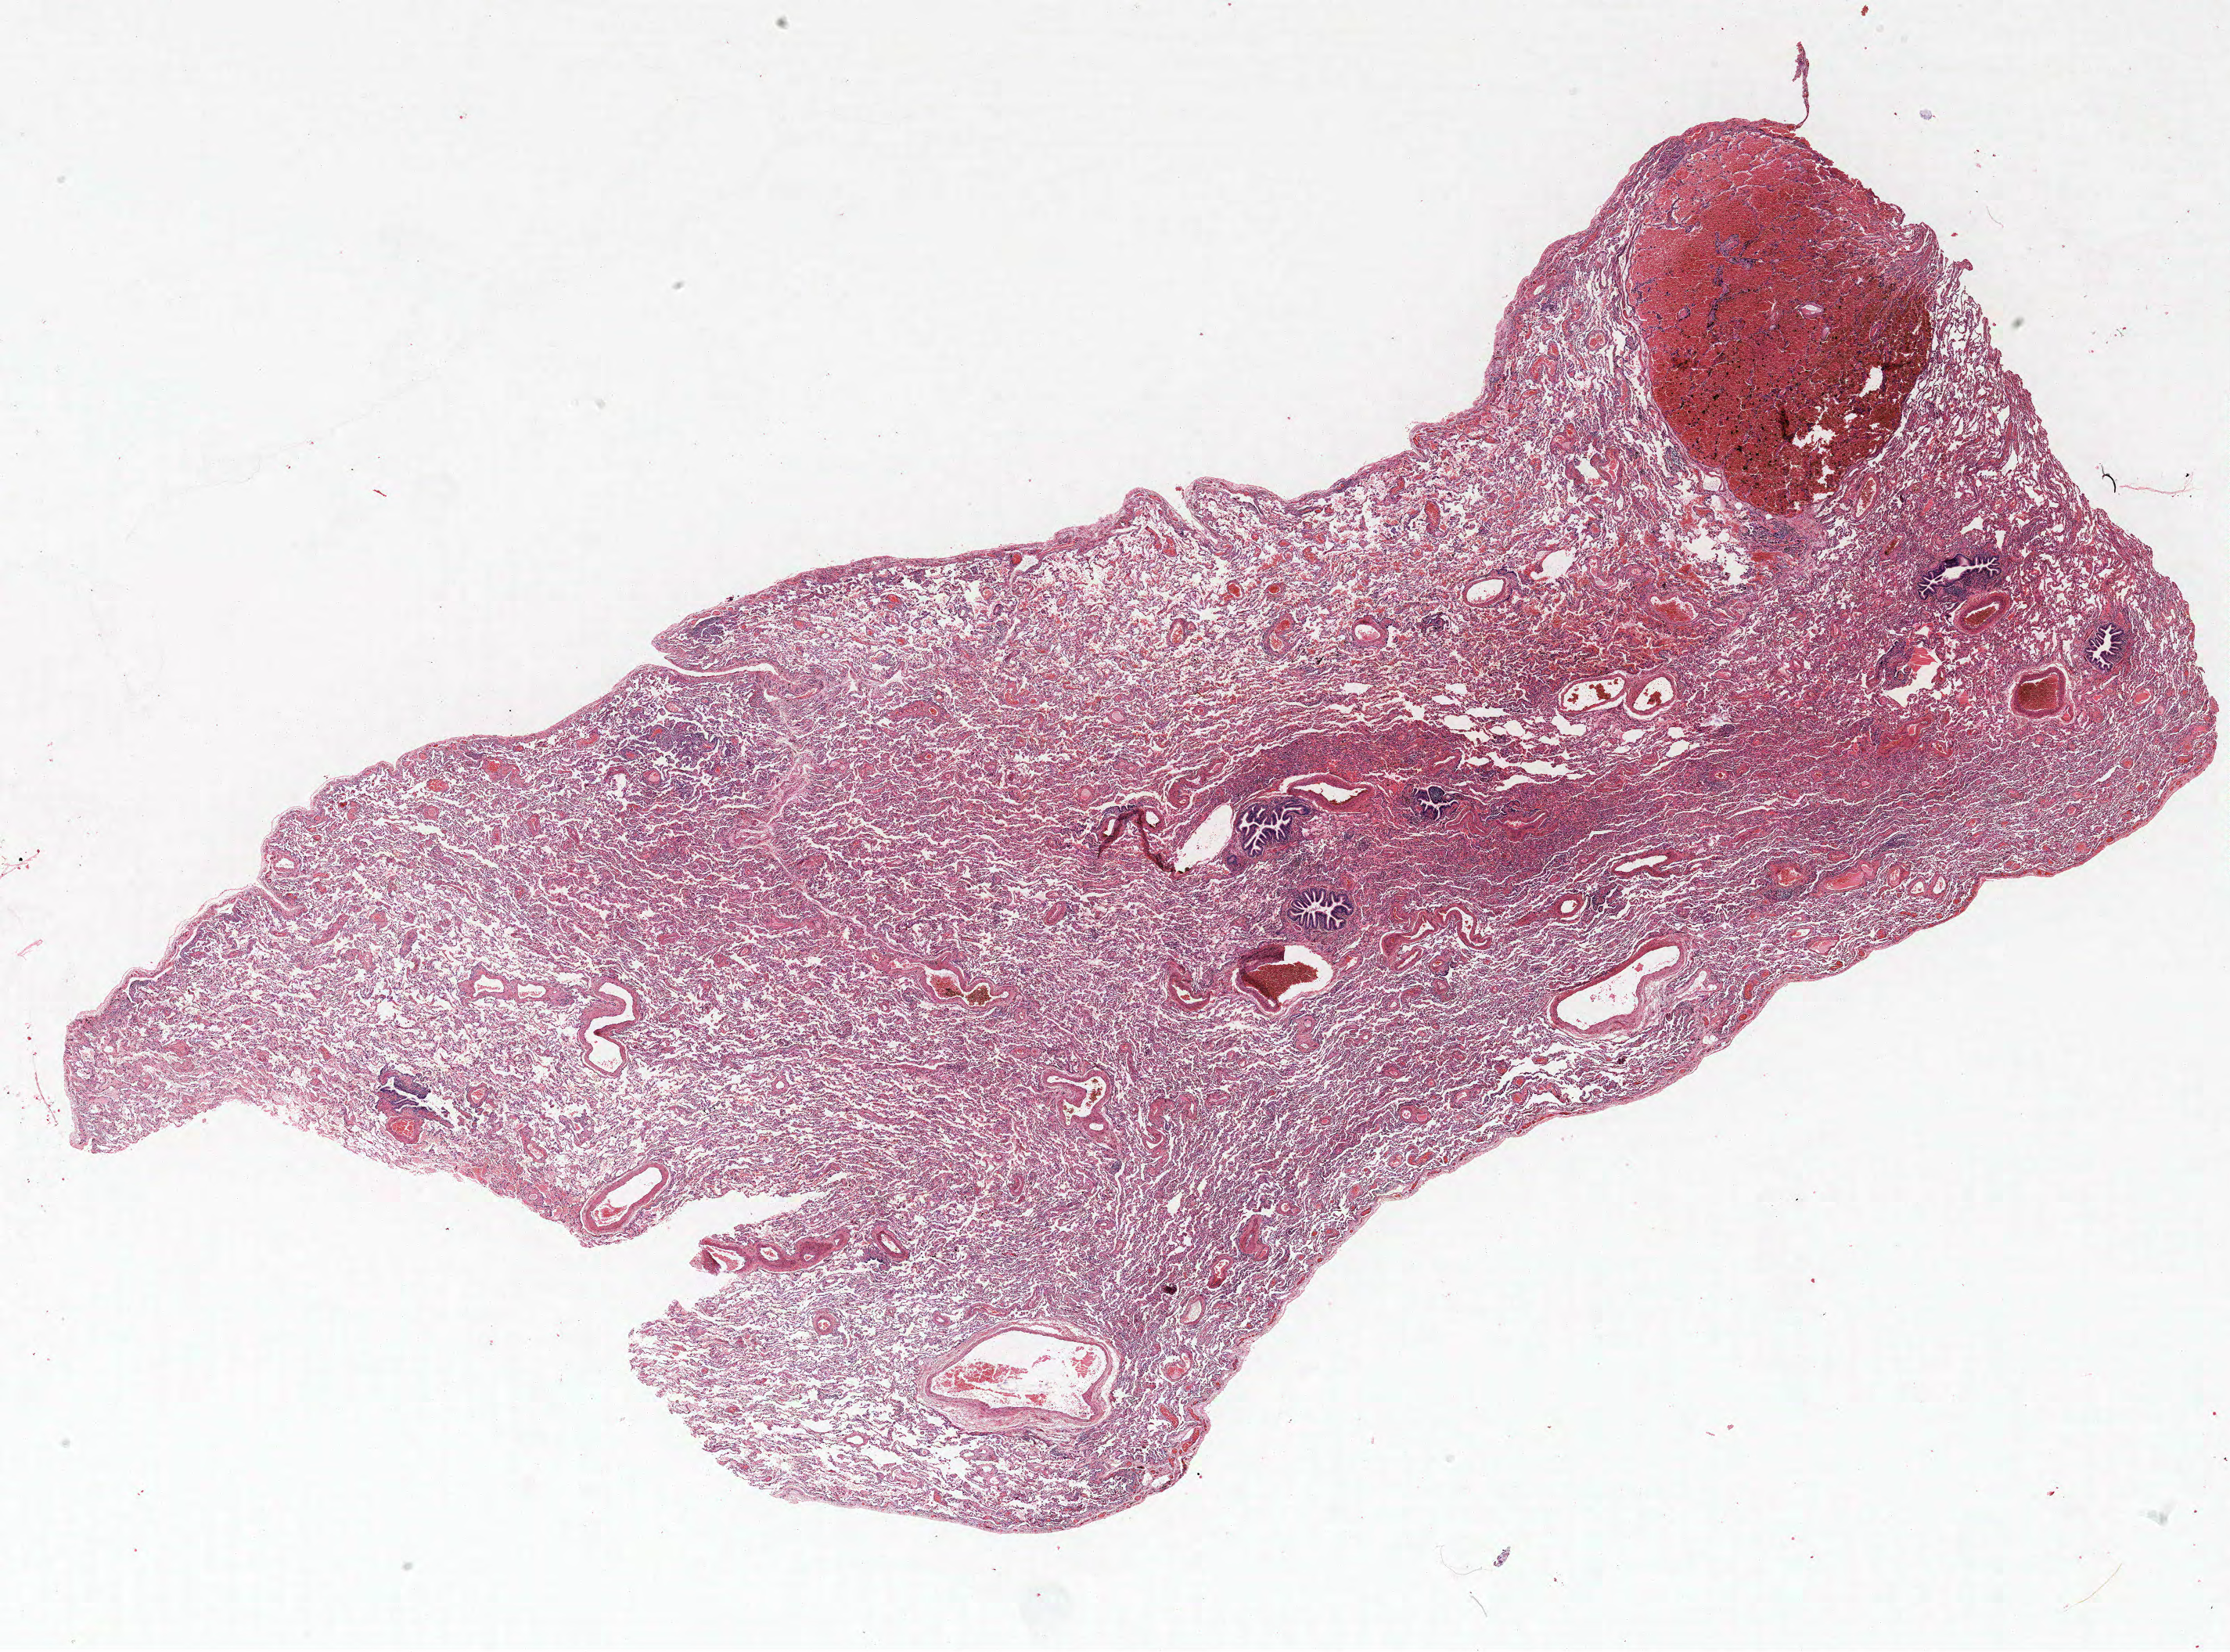
Whole-slide histology image, H&E-stained, shown as a low-resolution overview of the whole scanned area (about 22.8 x 16.9 mm, slide scanned at 40x), formalin-fixed paraffin-embedded (FFPE) section, lung. Male, age 55 at enrolment. Former smoker at enrolment.
Participant's lung-cancer diagnosis: Acinar cell carcinoma (ICD-O-3 8550/3). Note: participant had 2 primary lung cancers recorded; fields above describe the first.